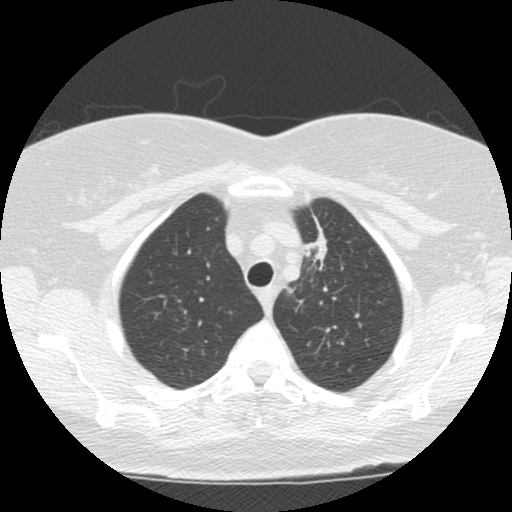
Low-dose screening chest CT, one axial slice; slice 96 of 120 in the series (ordered by position); reconstruction kernel STANDARD; lung window (W 1500 / L -600 HU); 2.5 mm slice thickness; 512 × 512 image matrix.
Annotated regions visible in this slice (outlined manually by an expert reader):
- lesion 1 (tumor, upper lobe of left lung): bounding box (x1, y1, x2, y2) in pixels: (303, 215, 327, 261)